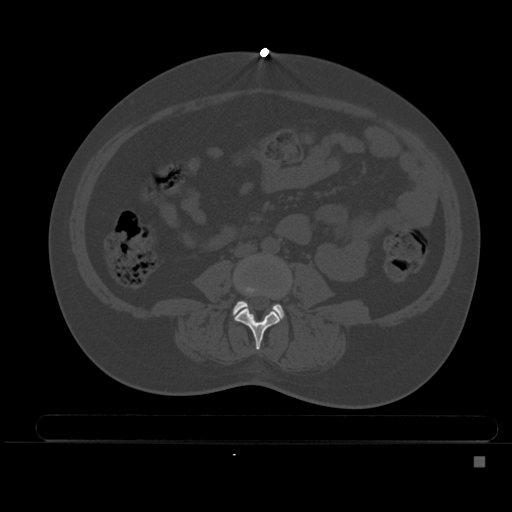
CT including the spine, one axial slice. Slice 141 of 495 in the series (ordered by position). Bone window (W 1800 / L 400 HU). 512 × 512 image matrix, field of view 404 × 404 mm. Female patient, age 33 years. Case-level facts recorded for this patient, not image findings: primary cancer: breast.
Outlined on this slice (semi-automatic segmentation, software-assisted and operator-edited):
- L3 vertebra: bounding box <235,286,288,350> (left, top, right, bottom; pixels)
- L4 vertebra: <233,288,284,318>